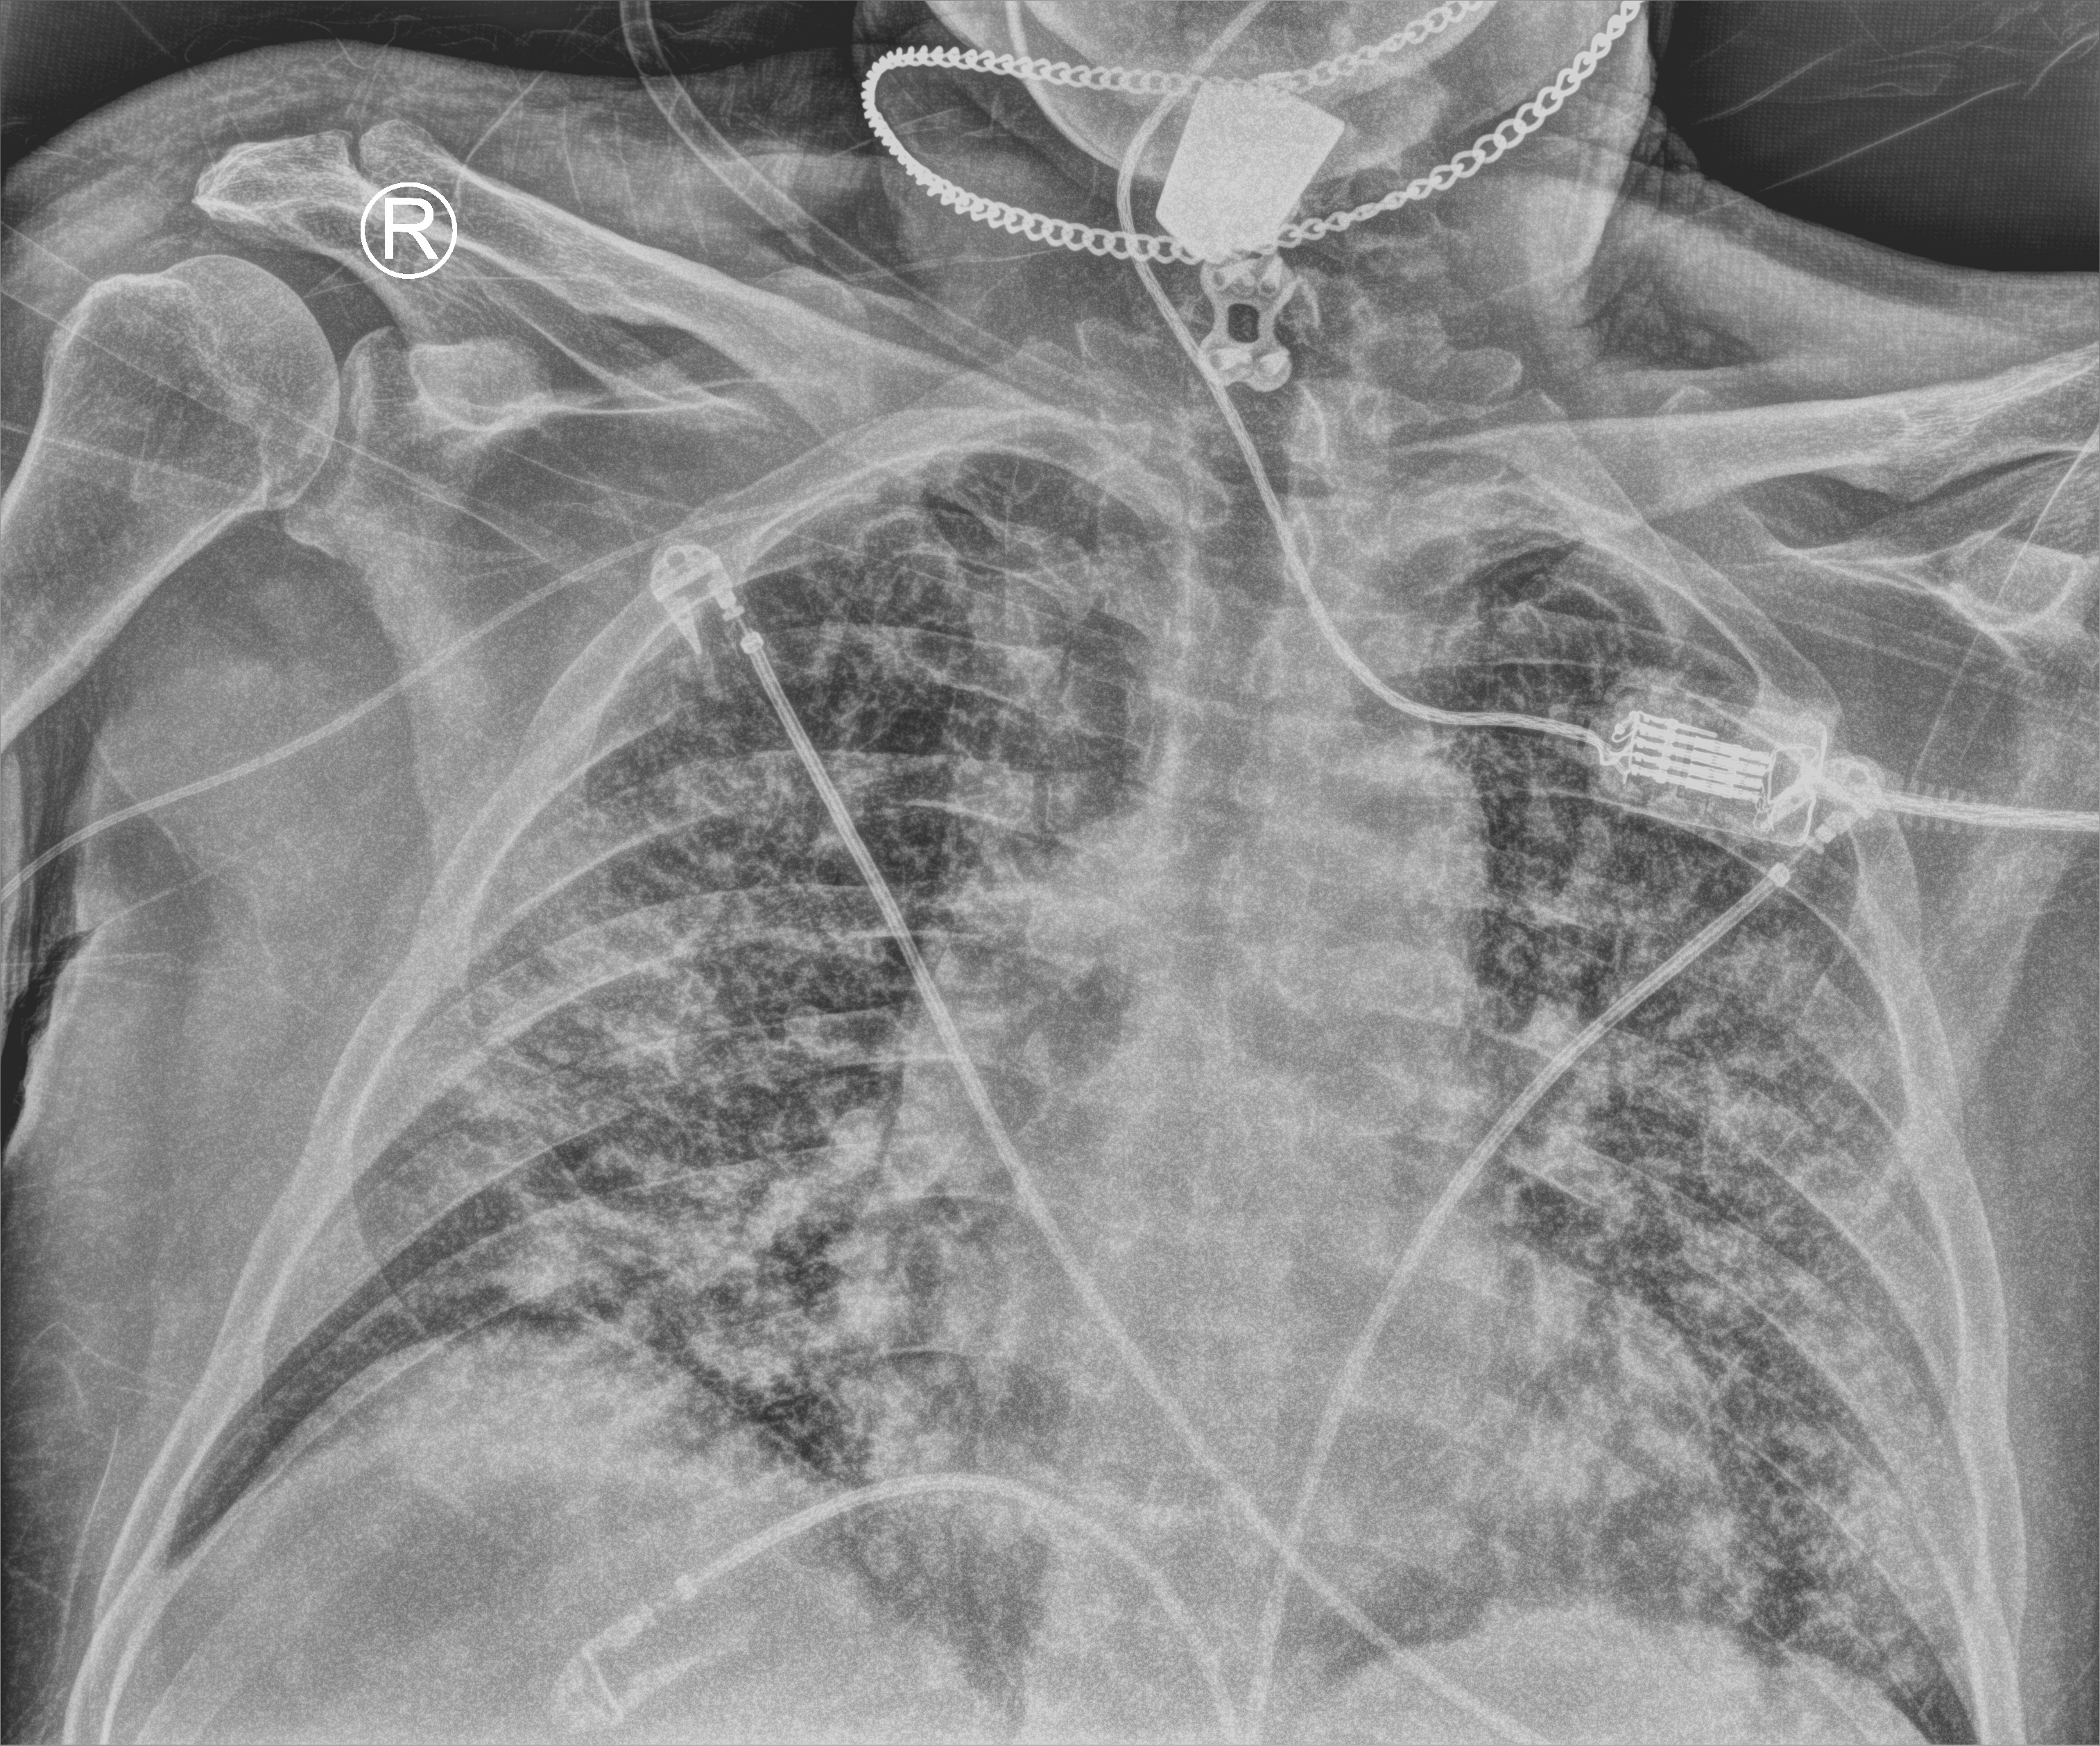
Chest X-ray (portable), anteroposterior (AP) projection. Male patient hospitalised with COVID-19, age 60–74 years.
Hospital-stay facts (about this admission, not read from this image; timing relative to this image not recorded): admitted to intensive care during this hospital stay: no; diabetes (admission record): no.